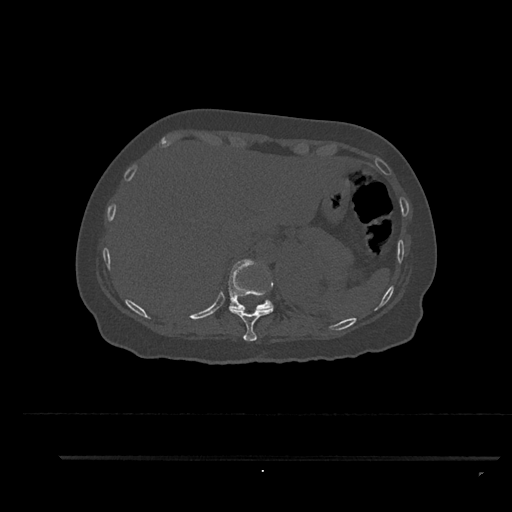
CT including the spine, one axial slice. Position 342 of 797 along the scan axis. Bone window (W 1800 / L 400 HU). 0.5 mm slice thickness. 512 × 512 image matrix, field of view 408 × 408 mm. Patient: female, 44 years. From the clinical record (not read from this slice): primary cancer: renal; vertebrae with lytic lesions (as recorded): L1.
Structures marked on this image (semi-automatically segmented with operator editing):
- T10 vertebra: bounding box (x1, y1, x2, y2) in pixels: (228, 306, 273, 341)
- T11 vertebra: (228, 259, 274, 311)